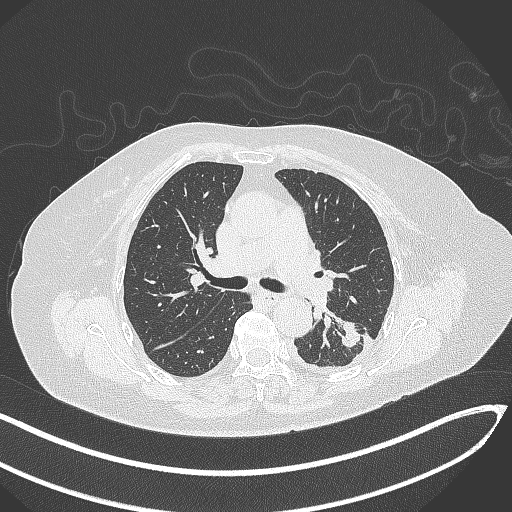
Chest CT, one axial slice; slice 196 of 270 in the series (ordered by position); reconstruction kernel B70f; lung window (W 1500 / L -600 HU); 512 × 512 image matrix. Female patient, age 76 years. Case-level facts recorded for this patient, not image findings: clinical TNM (as recorded): T1c N0 M0.
Structures marked on this image (bounding box drawn by a radiologist):
- lung tumour (recorded histology: adenocarcinoma): bounding box (x1, y1, x2, y2) in pixels: (333, 322, 362, 352)